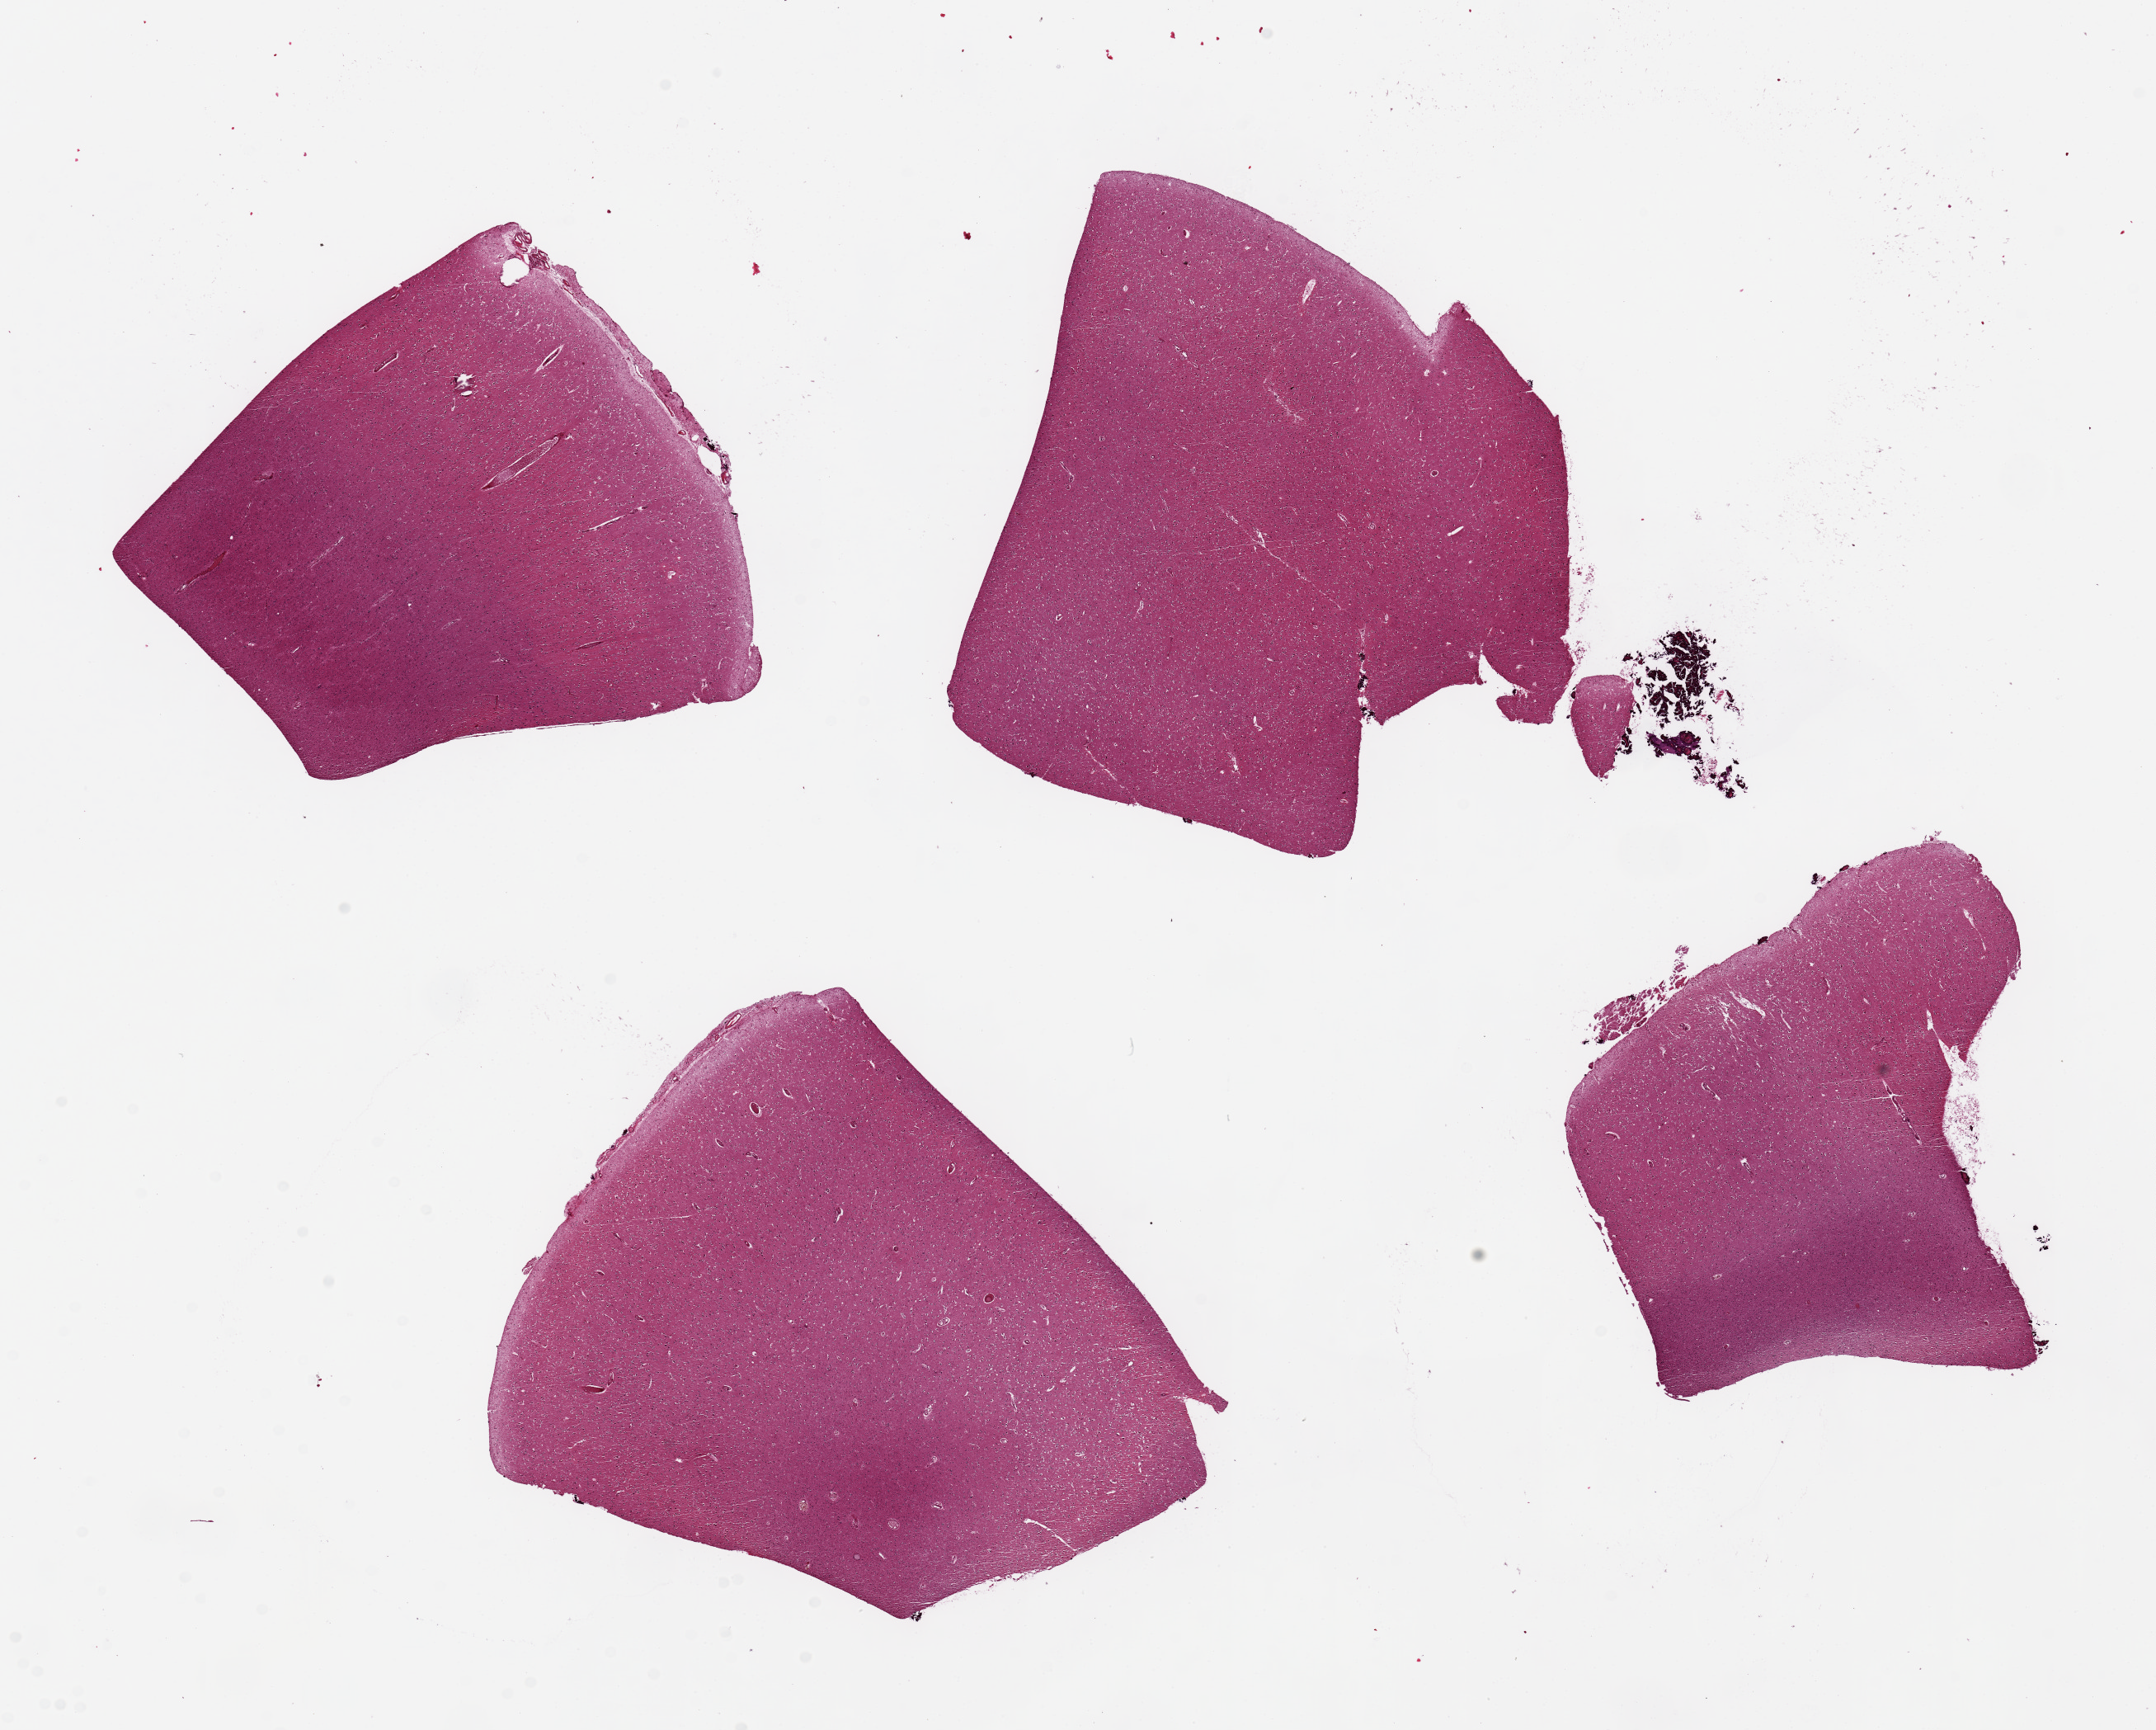
H&E whole-slide image, shown as a low-resolution overview of the whole scanned area (about 20.7 x 16.6 mm, slide scanned at 20x). PAXgene-fixed paraffin-embedded (PFPE) section. Section of cerebral cortex (target tissue). Tissue donor sample. Donor sex: female.
- review note (as recorded): 4 ~6x4mm aliquots. Some have a ~ 0.1mm layer of adherent pia arachnoid